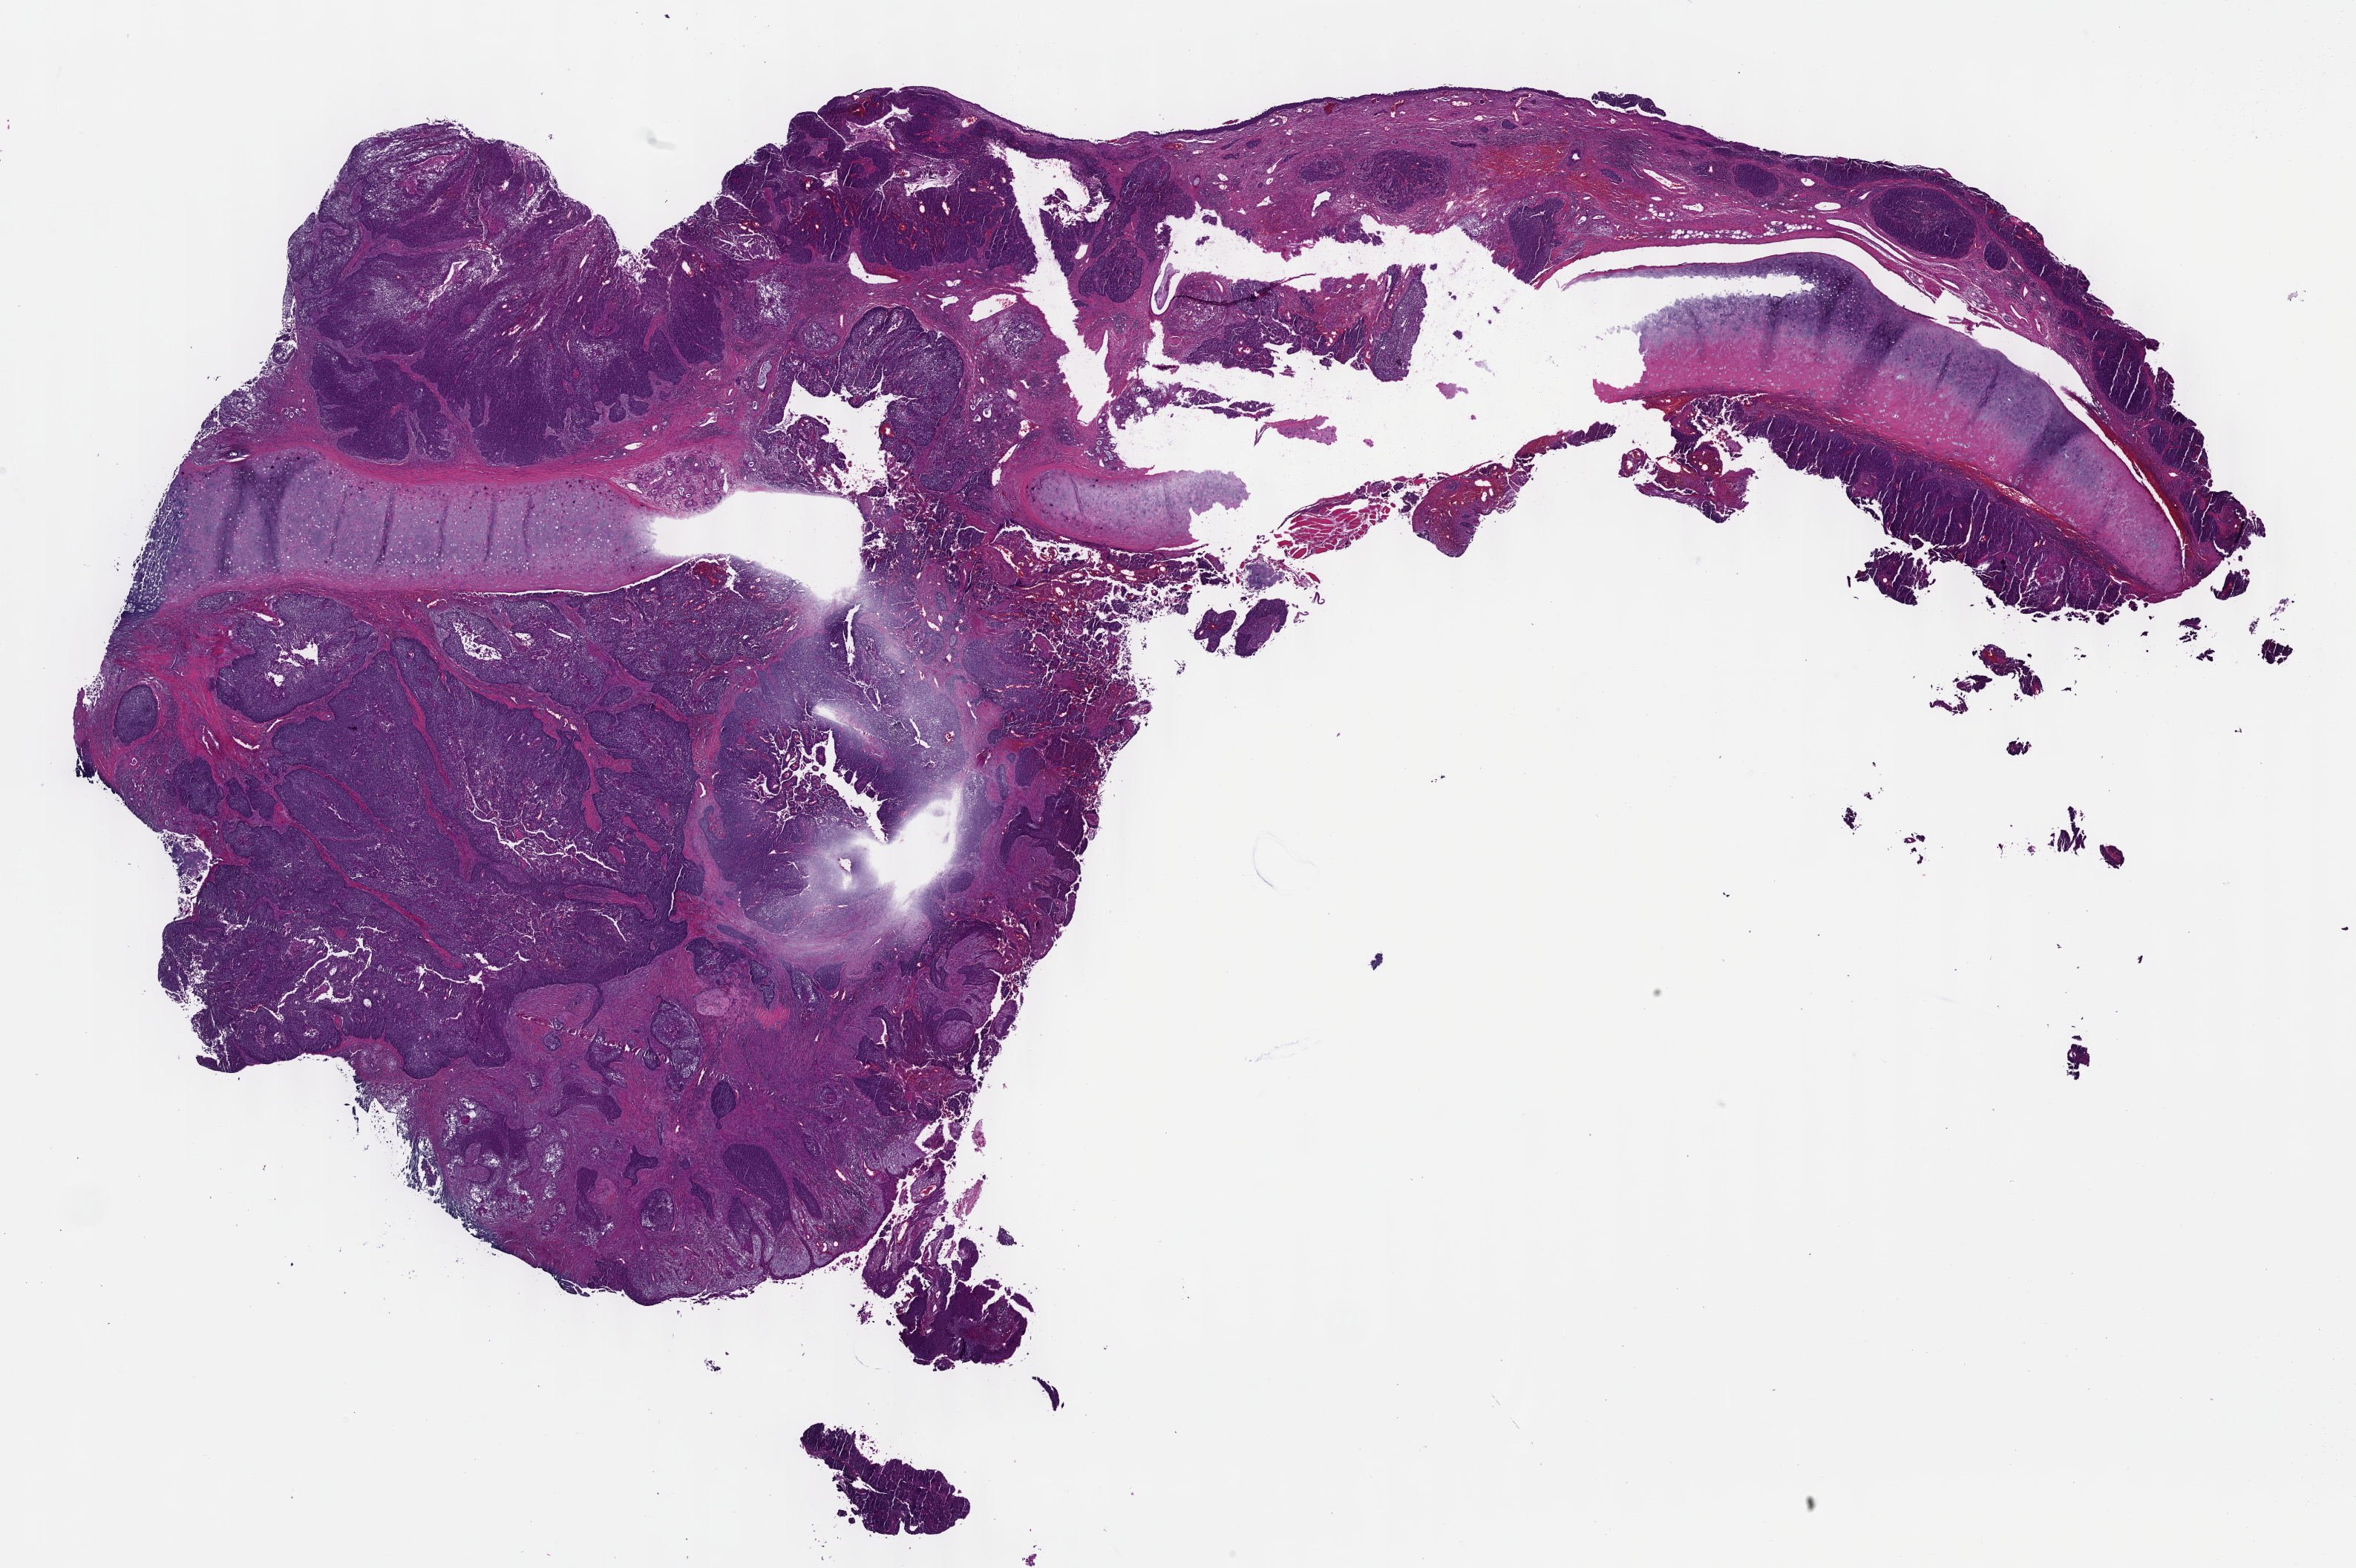
Whole-slide histology image, H&E, shown as a low-resolution overview of the whole scanned area (about 25.7 x 17.1 mm, slide scanned at 40x). FFPE section. Sample: primary tumour, head and neck. Male patient; age at initial diagnosis 60 years. Histologic grade: G3 (poorly differentiated).
- lymph nodes positive (case pathology): 2 of 12 examined
- TNM: T4a N2b
- AJCC pathologic stage: IVA
- histologic diagnosis: Squamous cell carcinoma, NOS